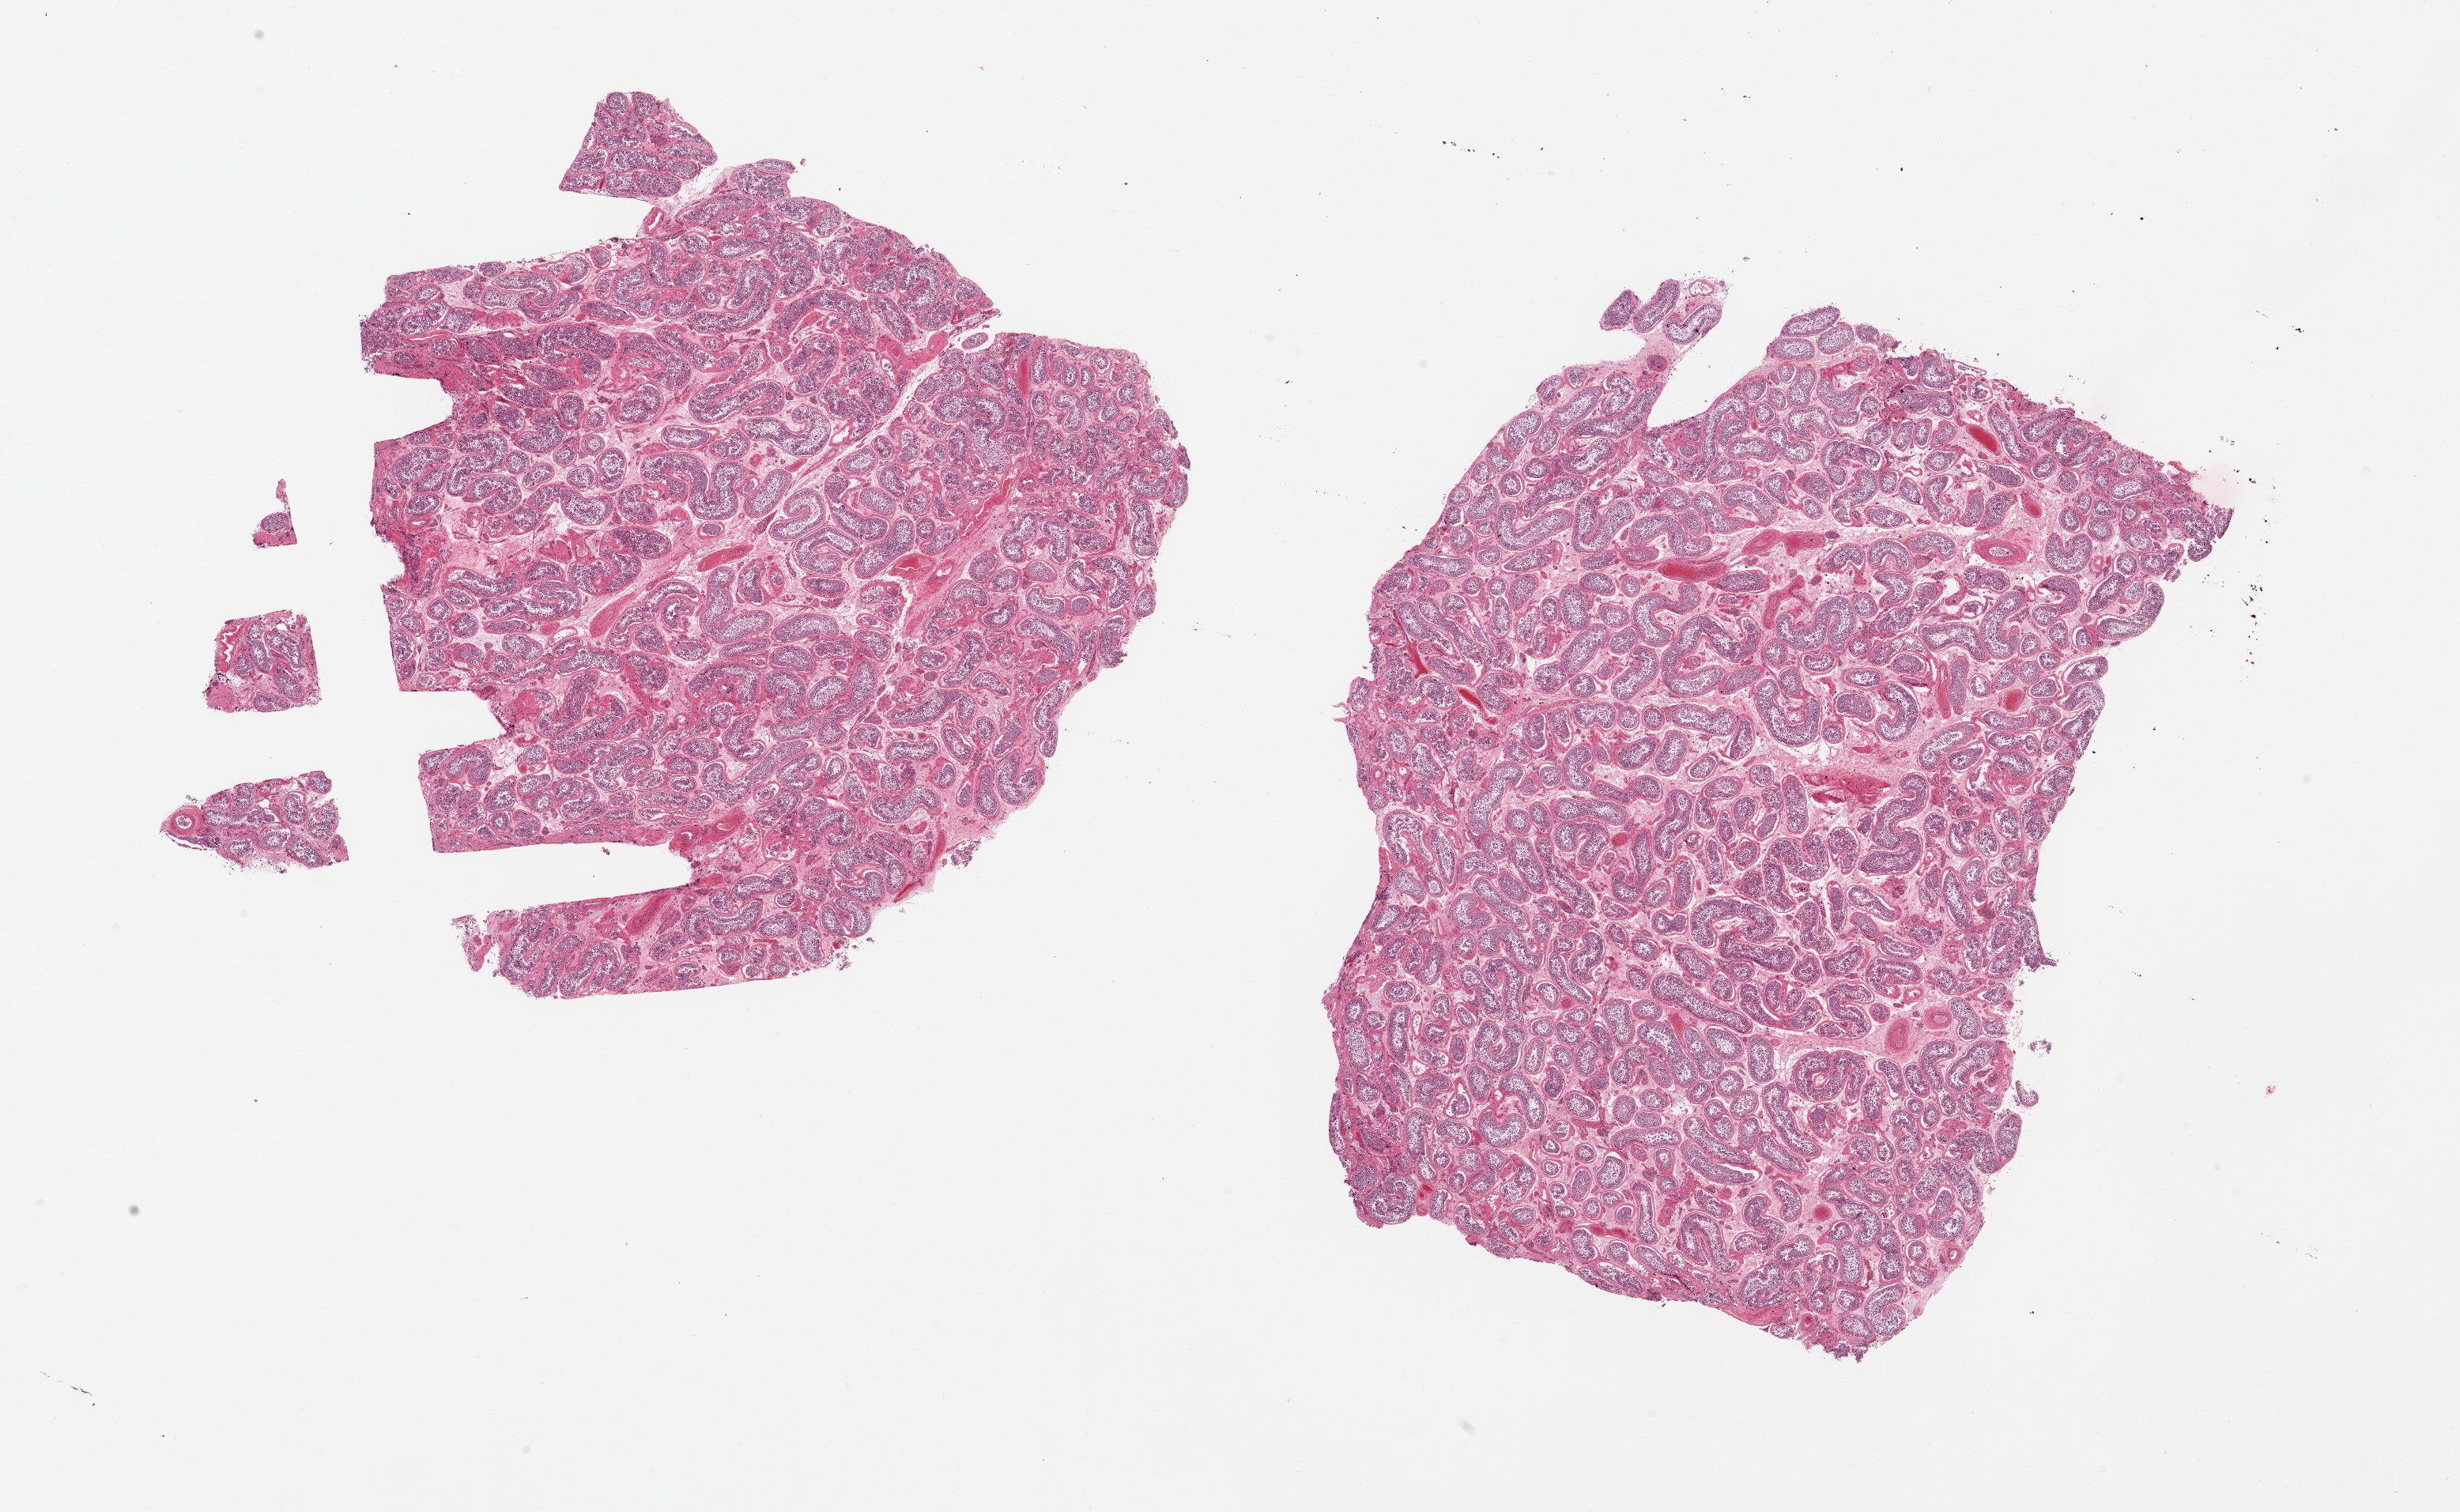
Whole-slide image, hematoxylin and eosin (H&E) stain — shown as a low-resolution overview of the whole scanned area (about 24.6 x 15.1 mm, from a 20x scan); PAXgene-fixed, paraffin-embedded tissue; target tissue: testis; tissue donor sample. Male donor.
Review note (as recorded): 2 pieces; spermatogenesis present.